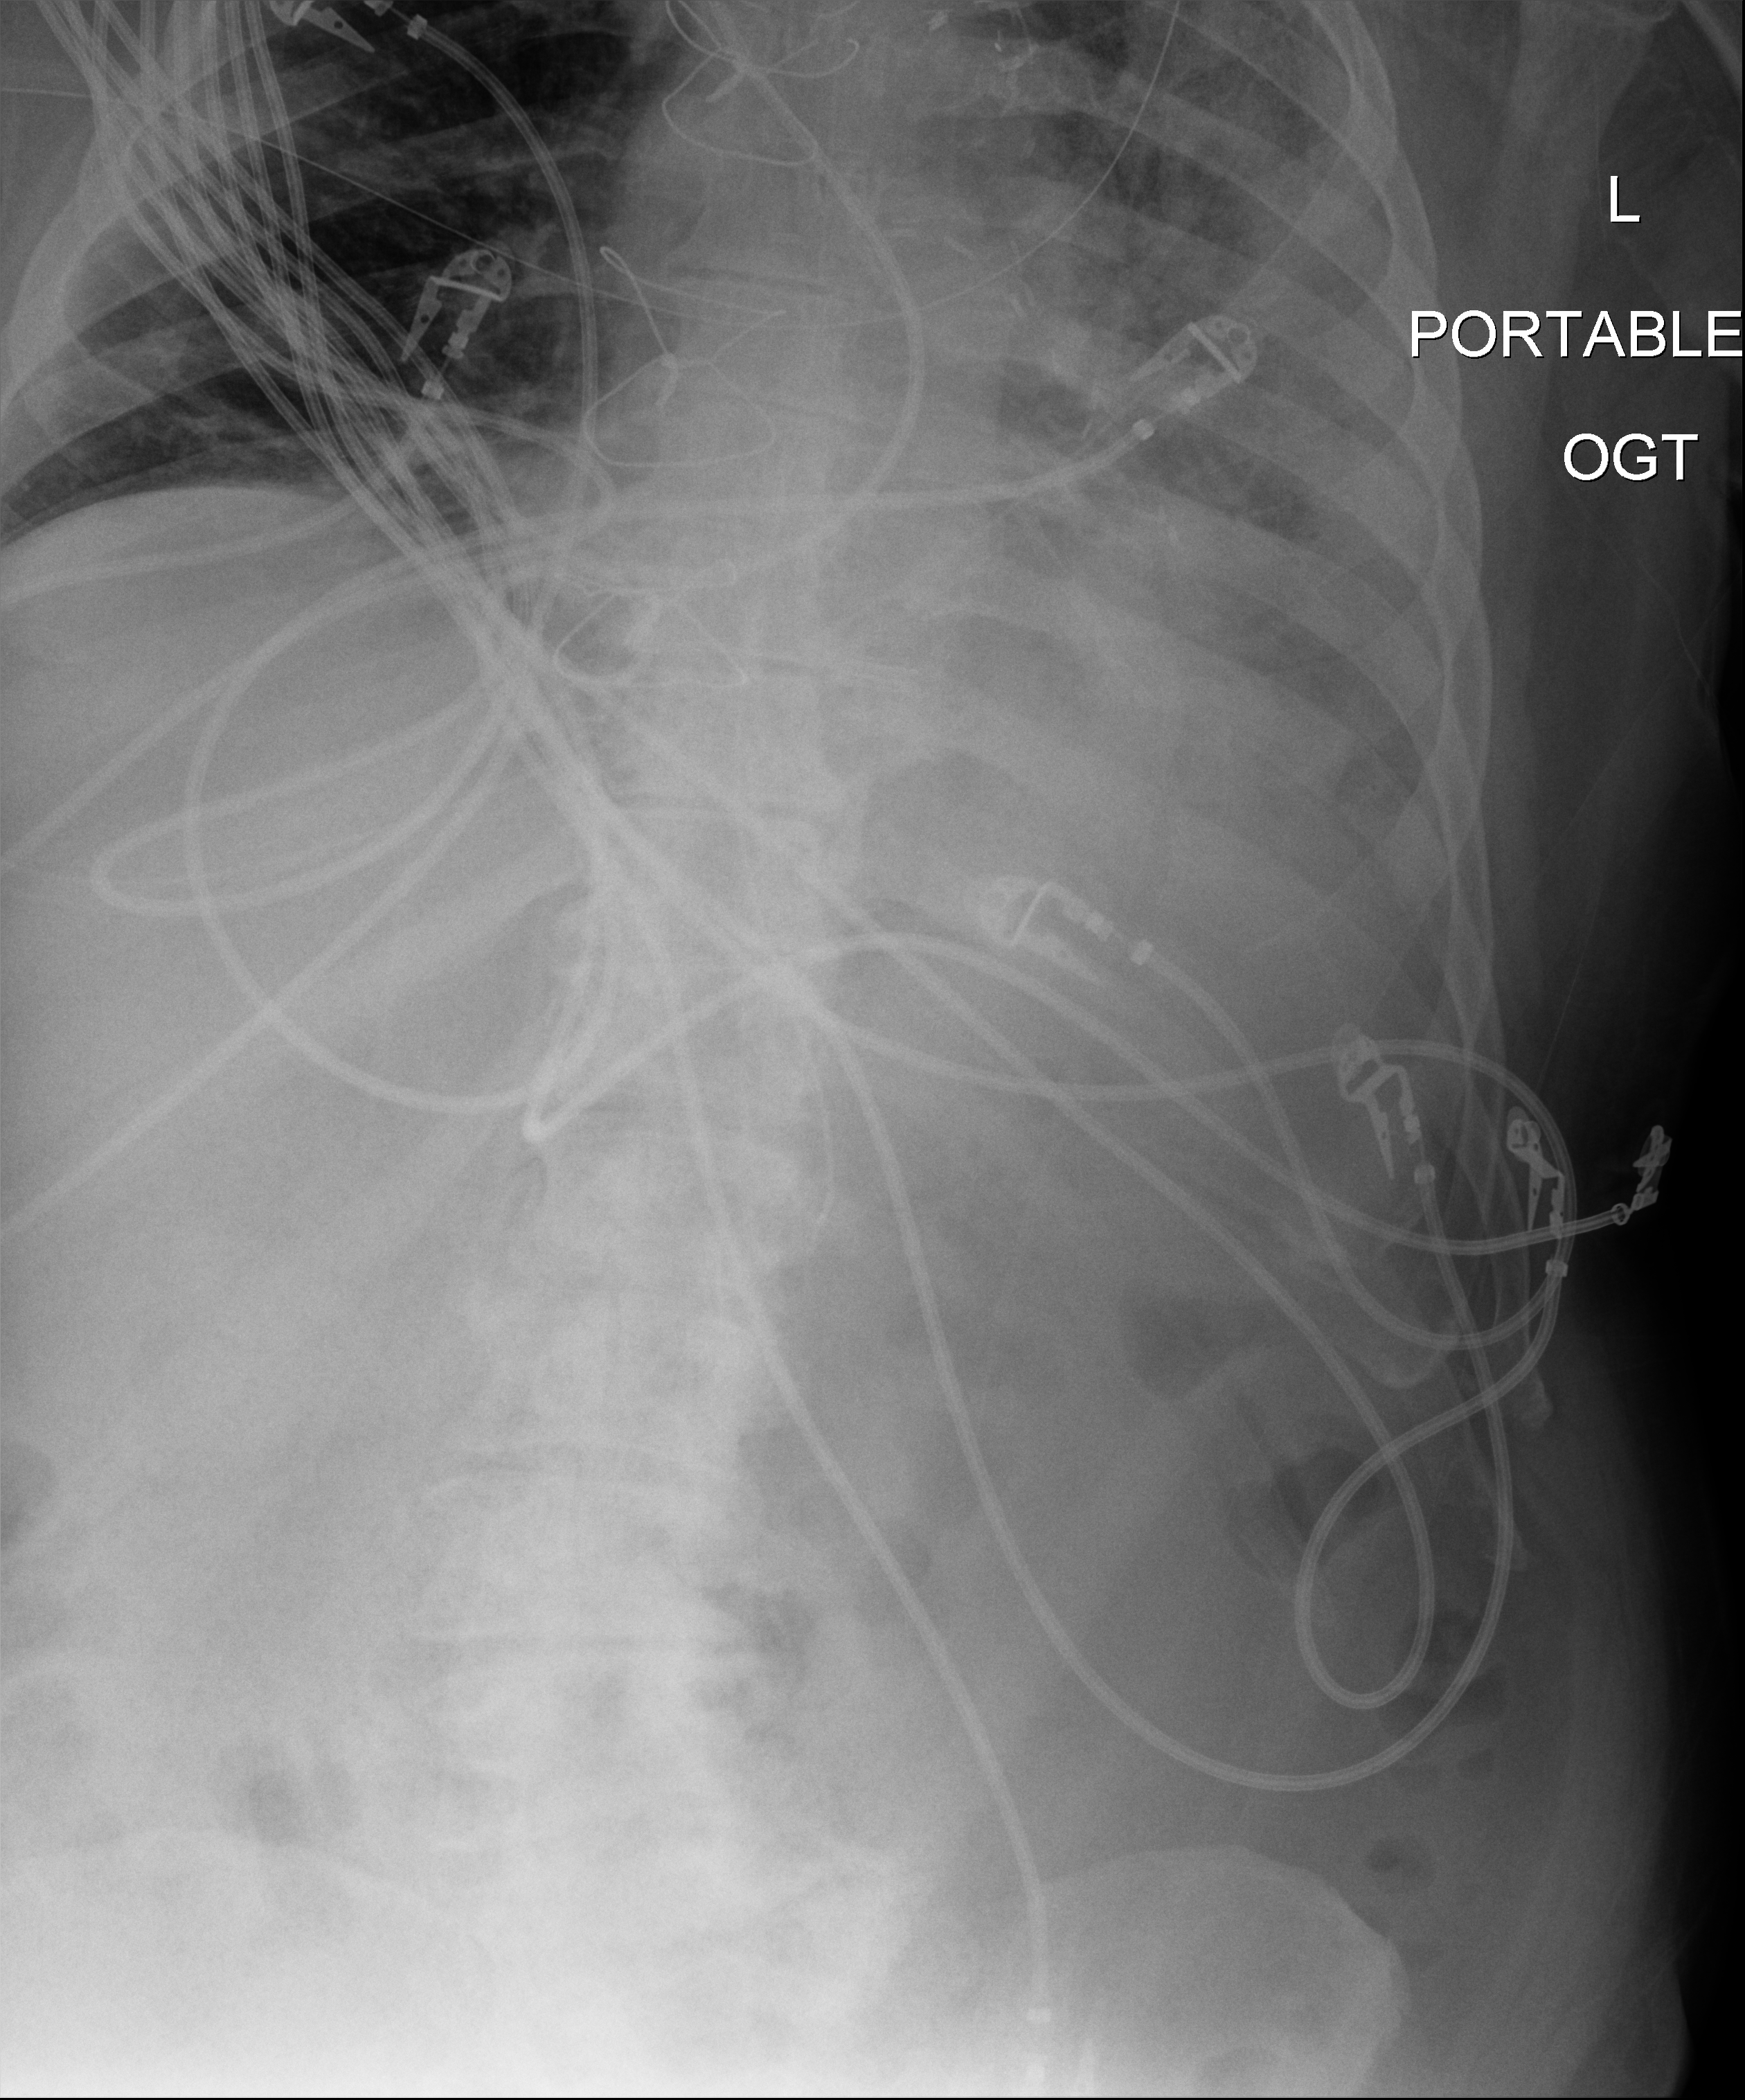
Bedside chest radiograph (digital radiography); anteroposterior (AP) projection. Patient hospitalised with COVID-19; male, aged 60–74 years.
Admission-level facts for this patient (not findings on this image; timing relative to this image not recorded): mechanically ventilated during this hospital stay: yes; hypertension (admission record): yes.